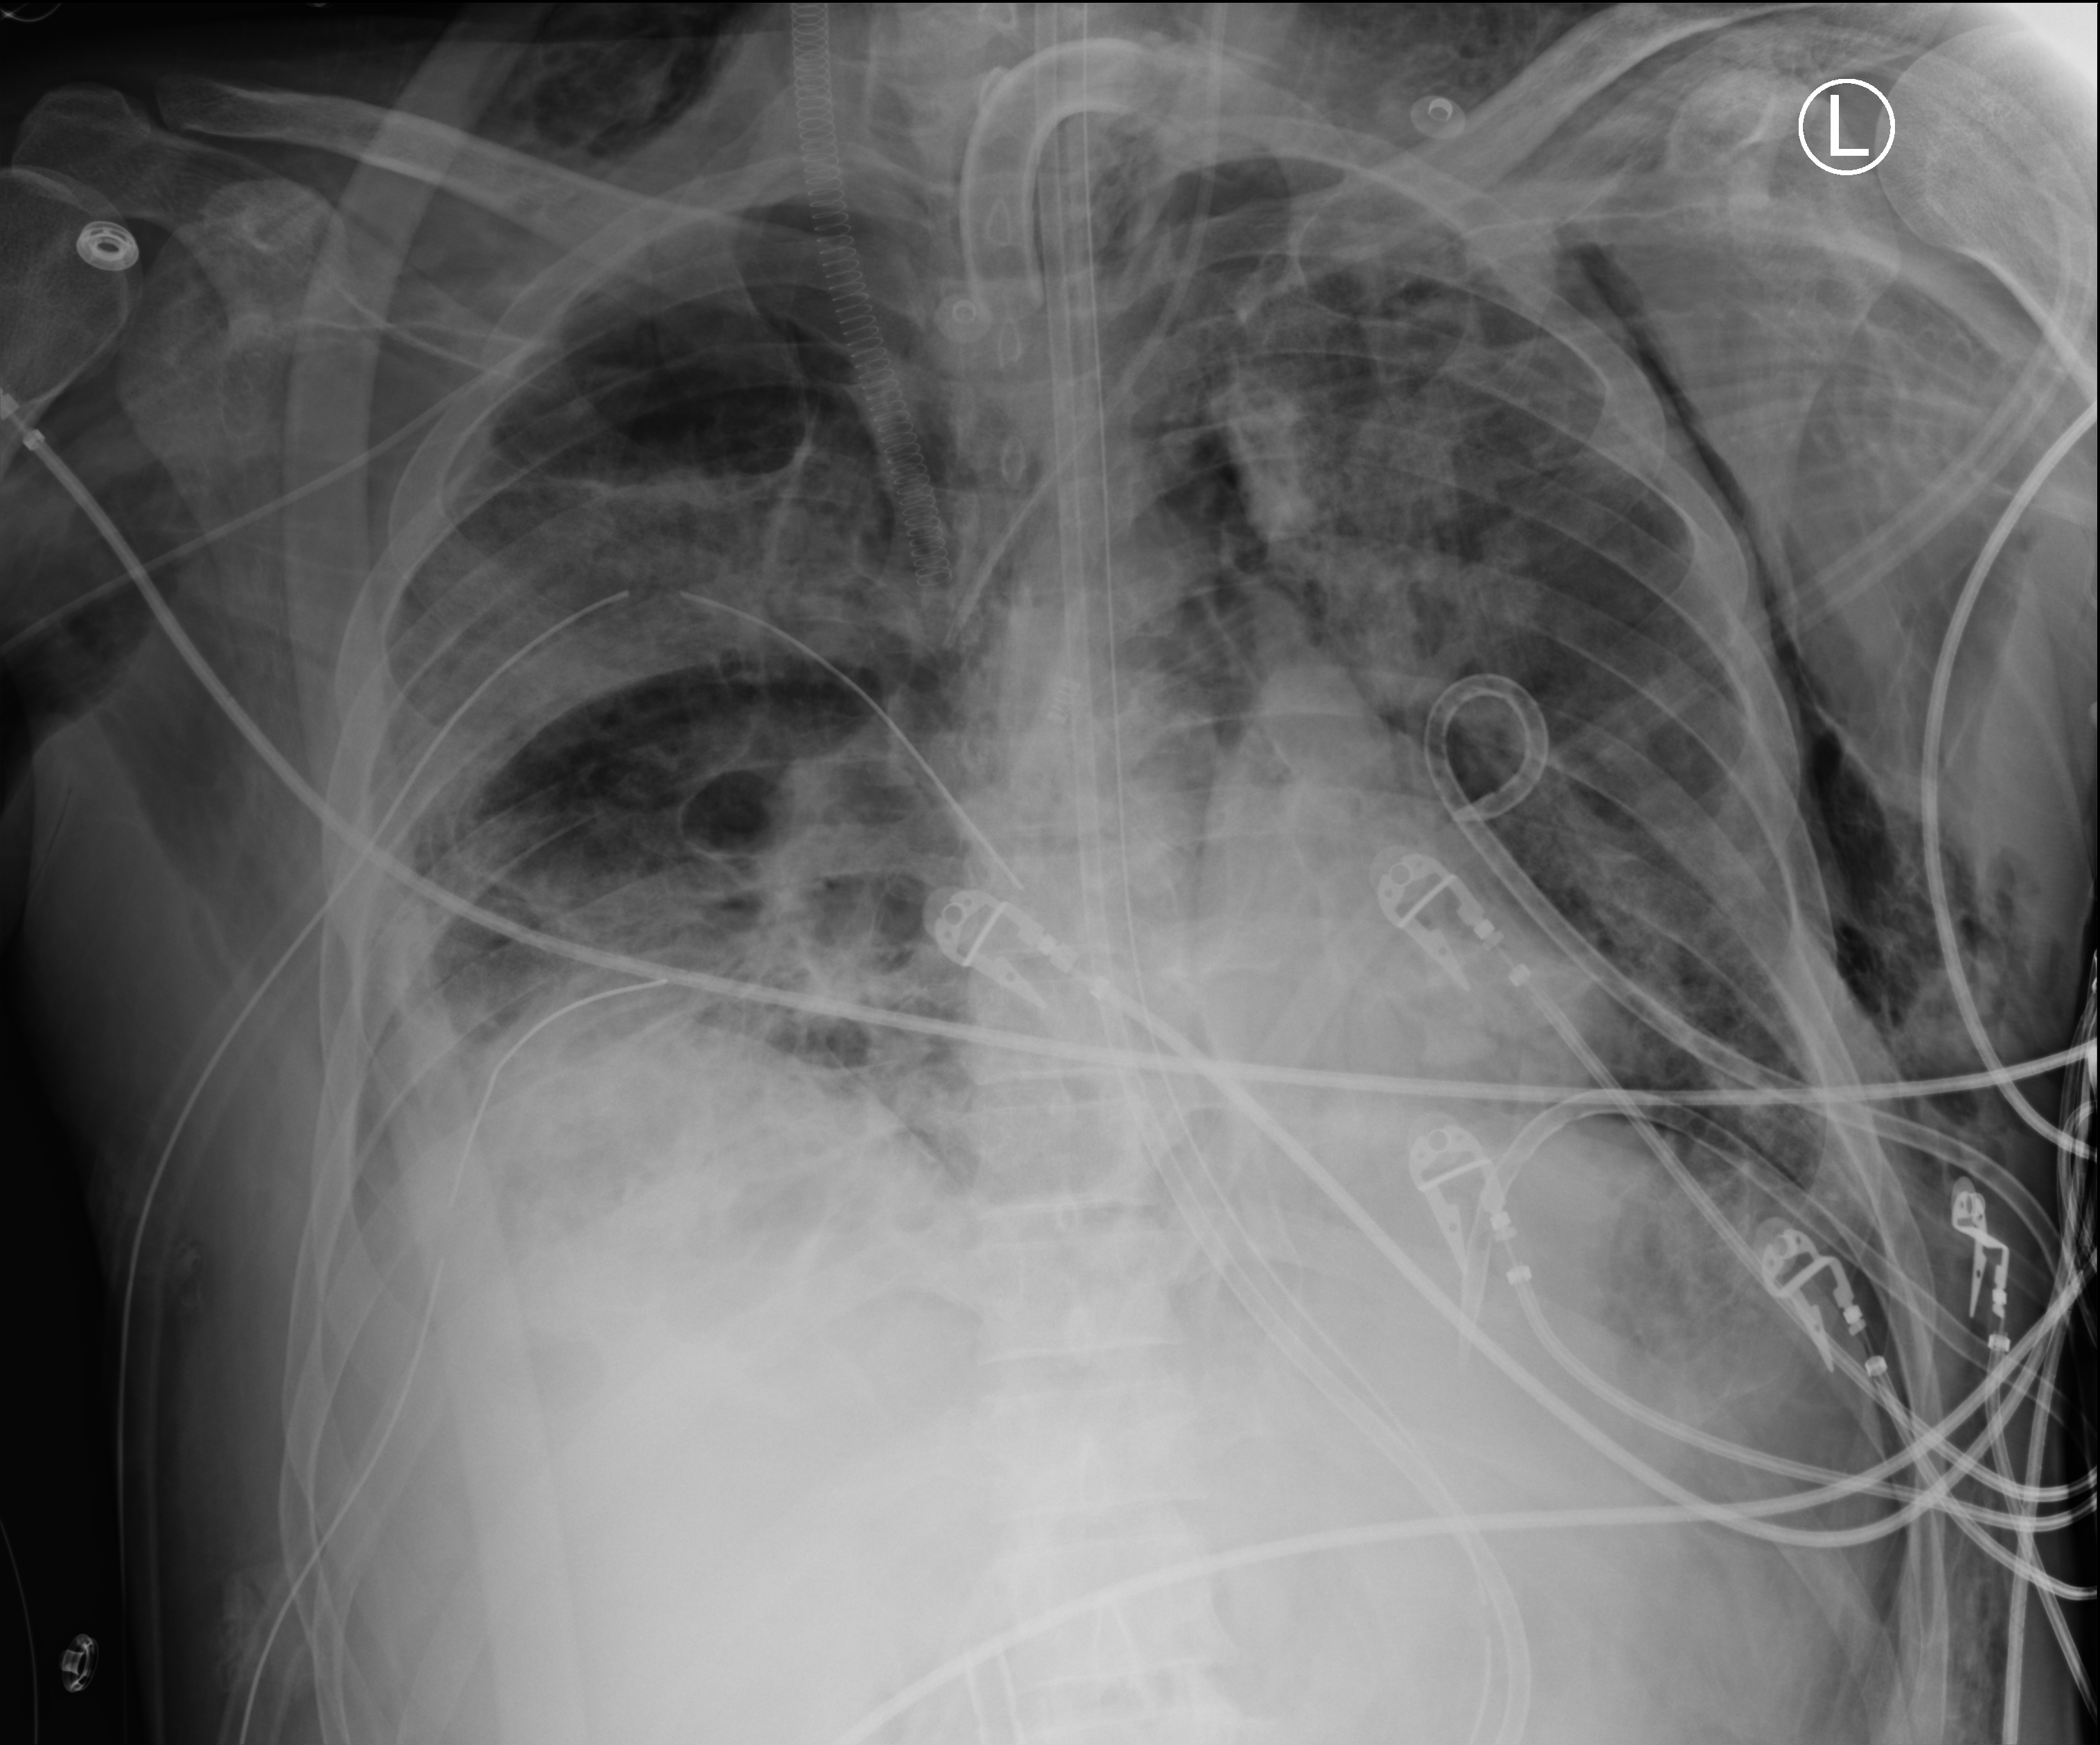
Portable chest radiograph; anteroposterior (AP) projection. Patient hospitalised with COVID-19, aged 18–59 years.
Admission-level facts for this patient (not findings on this image; timing relative to this image not recorded):
- mechanically ventilated during this hospital stay: yes